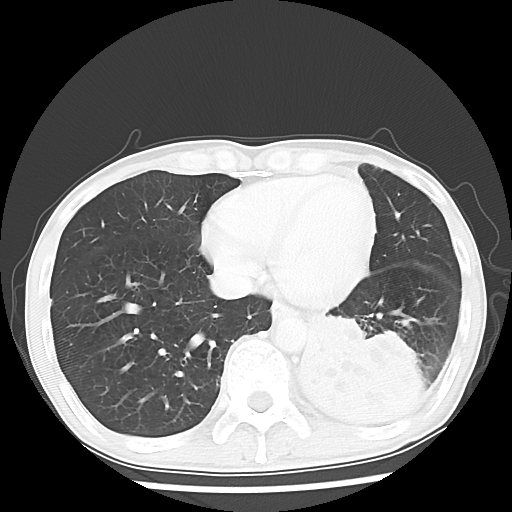
Chest CT, one axial slice; position 18 of 64 along the scan axis; lung window (W 1500 / L -600 HU); 5 mm slice thickness; 512 × 512 image matrix. Male patient, age 68 years. Case-level facts recorded for this patient, not image findings: clinical TNM (as recorded): T4 N0 M0.
Outlined on this slice (rectangle marked by the reading radiologist):
- lung tumour (recorded histology: squamous cell carcinoma): bounding box <296,309,428,439> (left, top, right, bottom; pixels)